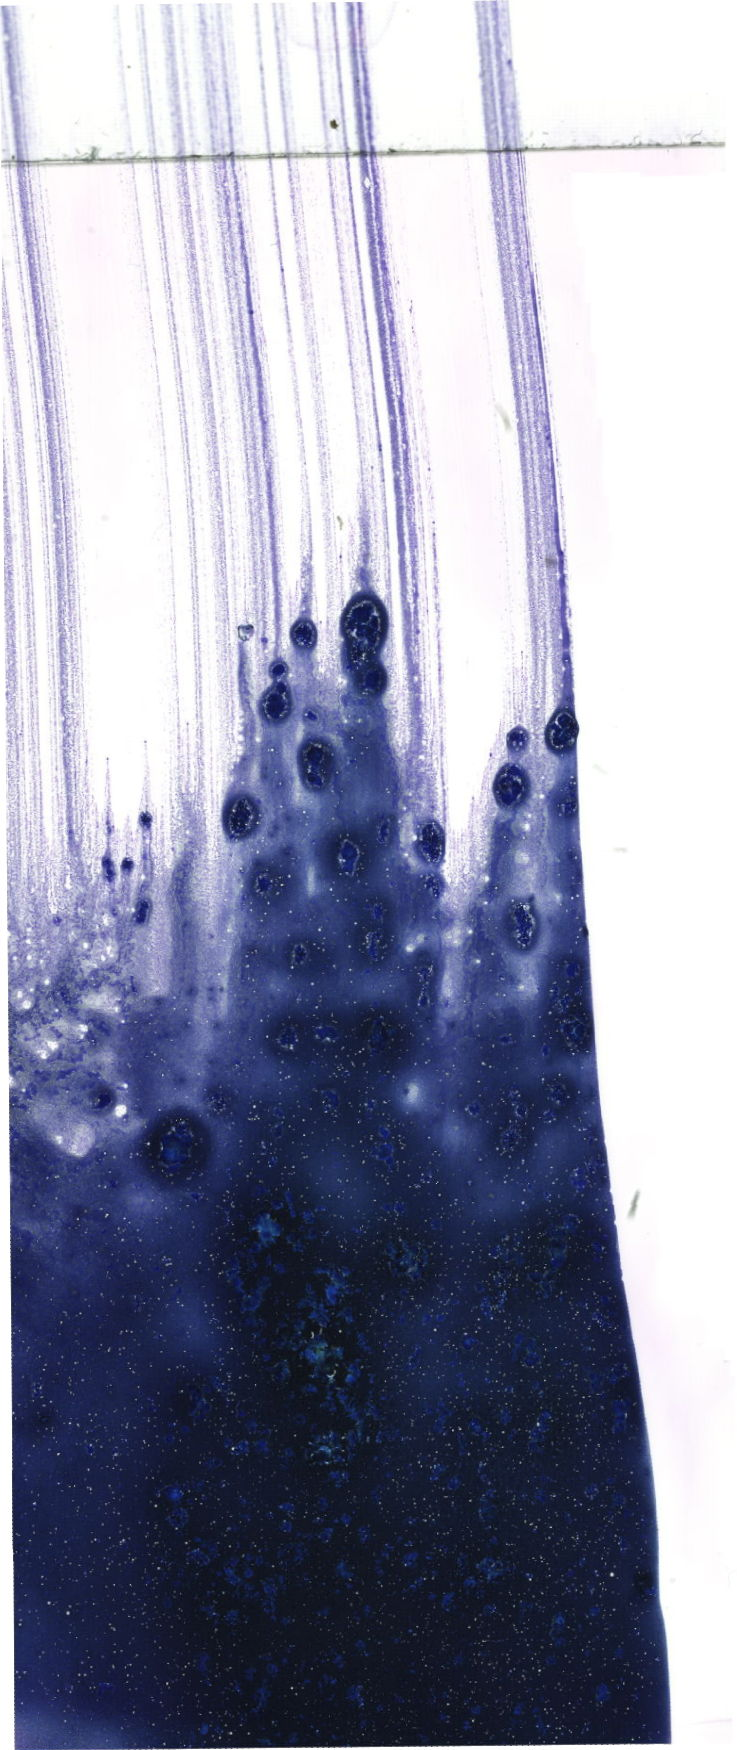
Whole-slide image of a May-Grünwald-Giemsa (MGG)-stained bone marrow aspirate smear — a low-resolution overview of the entire scanned area, about 20.9 x 49.6 mm. Male patient.
Diagnosis: T Acute Lymphoblastic Leukemia.